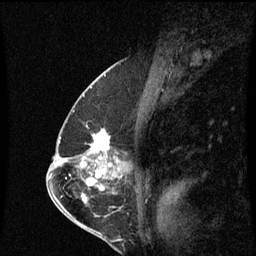
Breast MRI (dynamic contrast-enhanced), one sagittal slice. Slice 35 of 60 in the series (ordered by position). Dynamic contrast-enhanced series, image 2 of 3 at this slice position (ordered by acquisition). 1.5 T. TE 4.2 ms, TR 8.9 ms. 2 mm slice thickness. 256 × 256 image matrix, field of view 200 × 200 mm. Female patient, age 57 years. Case-level facts recorded for this patient, not image findings: setting: breast cancer imaged before/during neoadjuvant chemotherapy; receptor status: HR-positive, HER2-negative.
Structures marked on this image (semi-automatically segmented with operator editing):
- analysis volume of interest (the breast-tissue region the enhancement analysis was run in; not a lesion): bounding box <83,132,116,159> (left, top, right, bottom; pixels)
- tumour enhancement mask (voxels above the 70 % enhancement threshold inside the analysis volume of interest): <94,132,108,159>